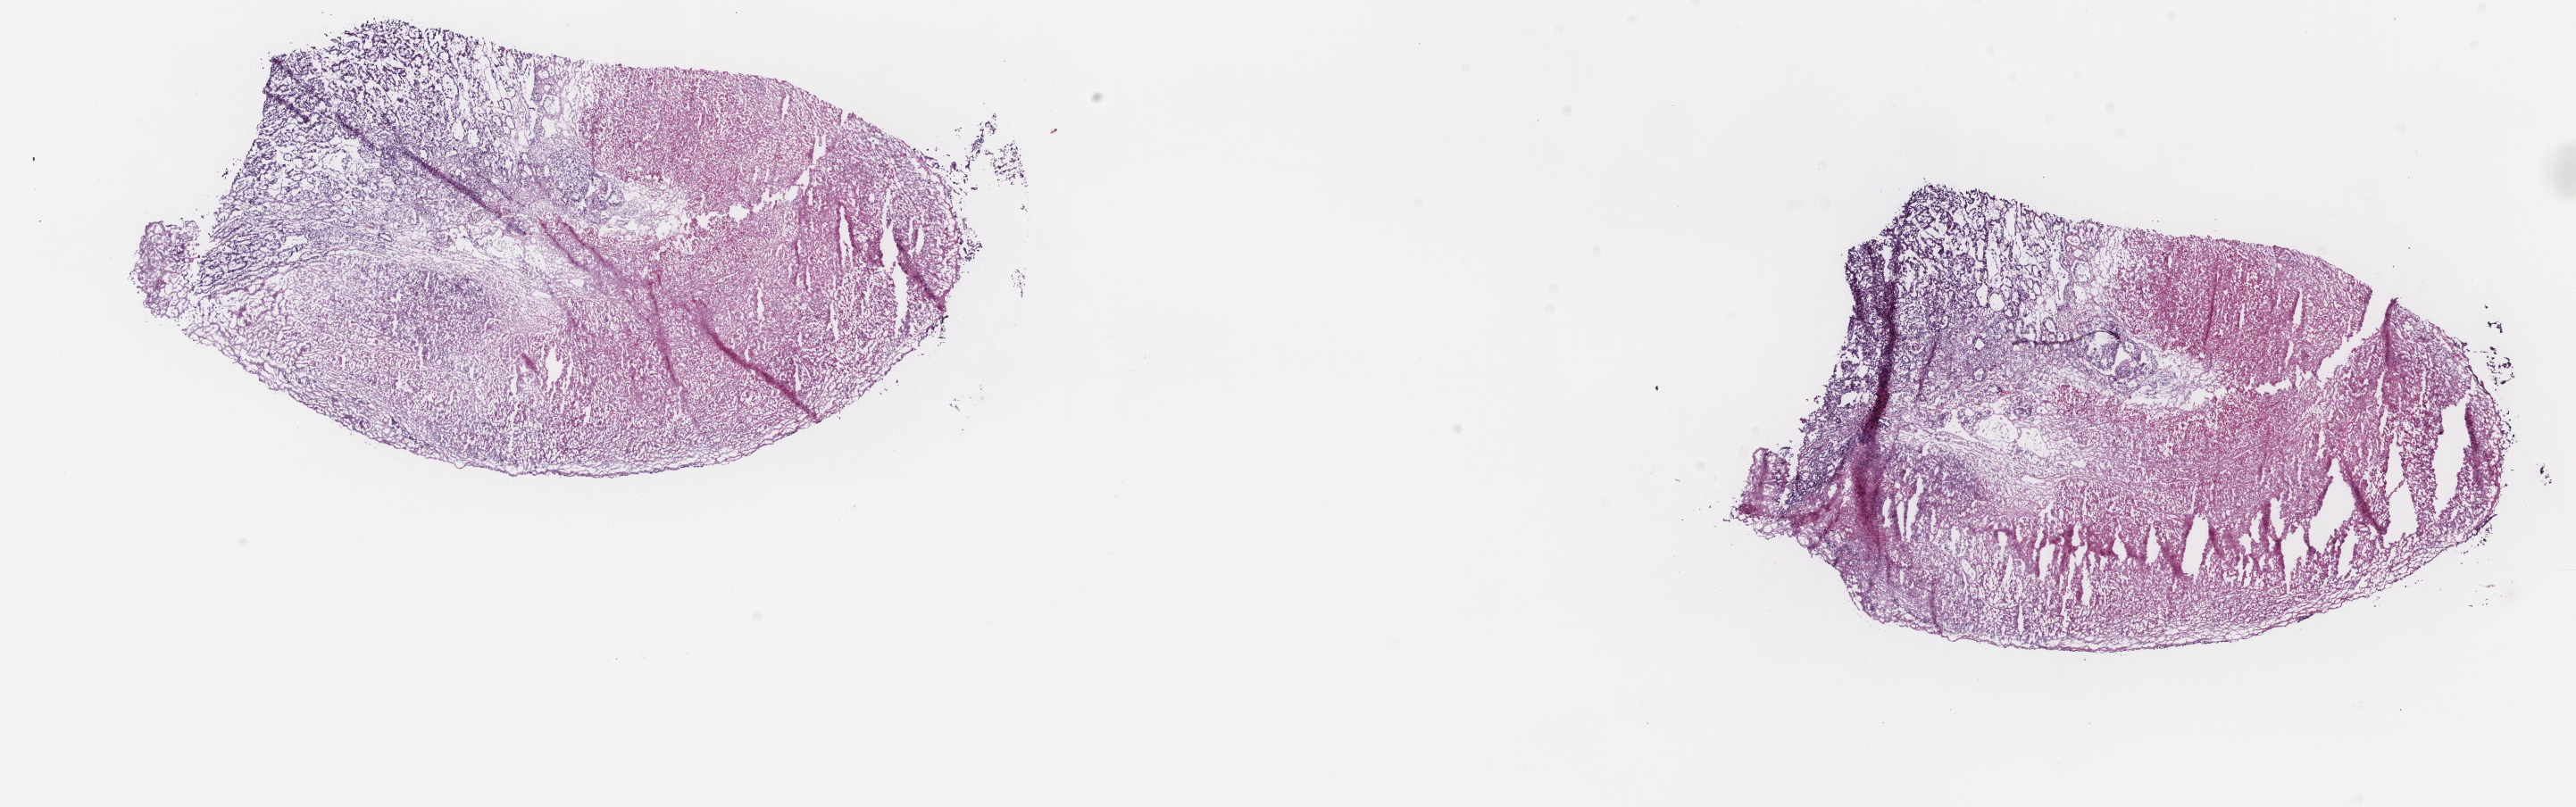
Digitized Hematoxylin and eosin (H&E) stained tissue section (whole slide), low-resolution overview of the scanned area, about 22.9 x 7.2 mm. Frozen section from the top of the tissue portion. Primary tumour sample from the uterus. Patient: female, age at initial diagnosis 75 years.
Pathologic diagnosis: Serous cystadenocarcinoma, NOS.